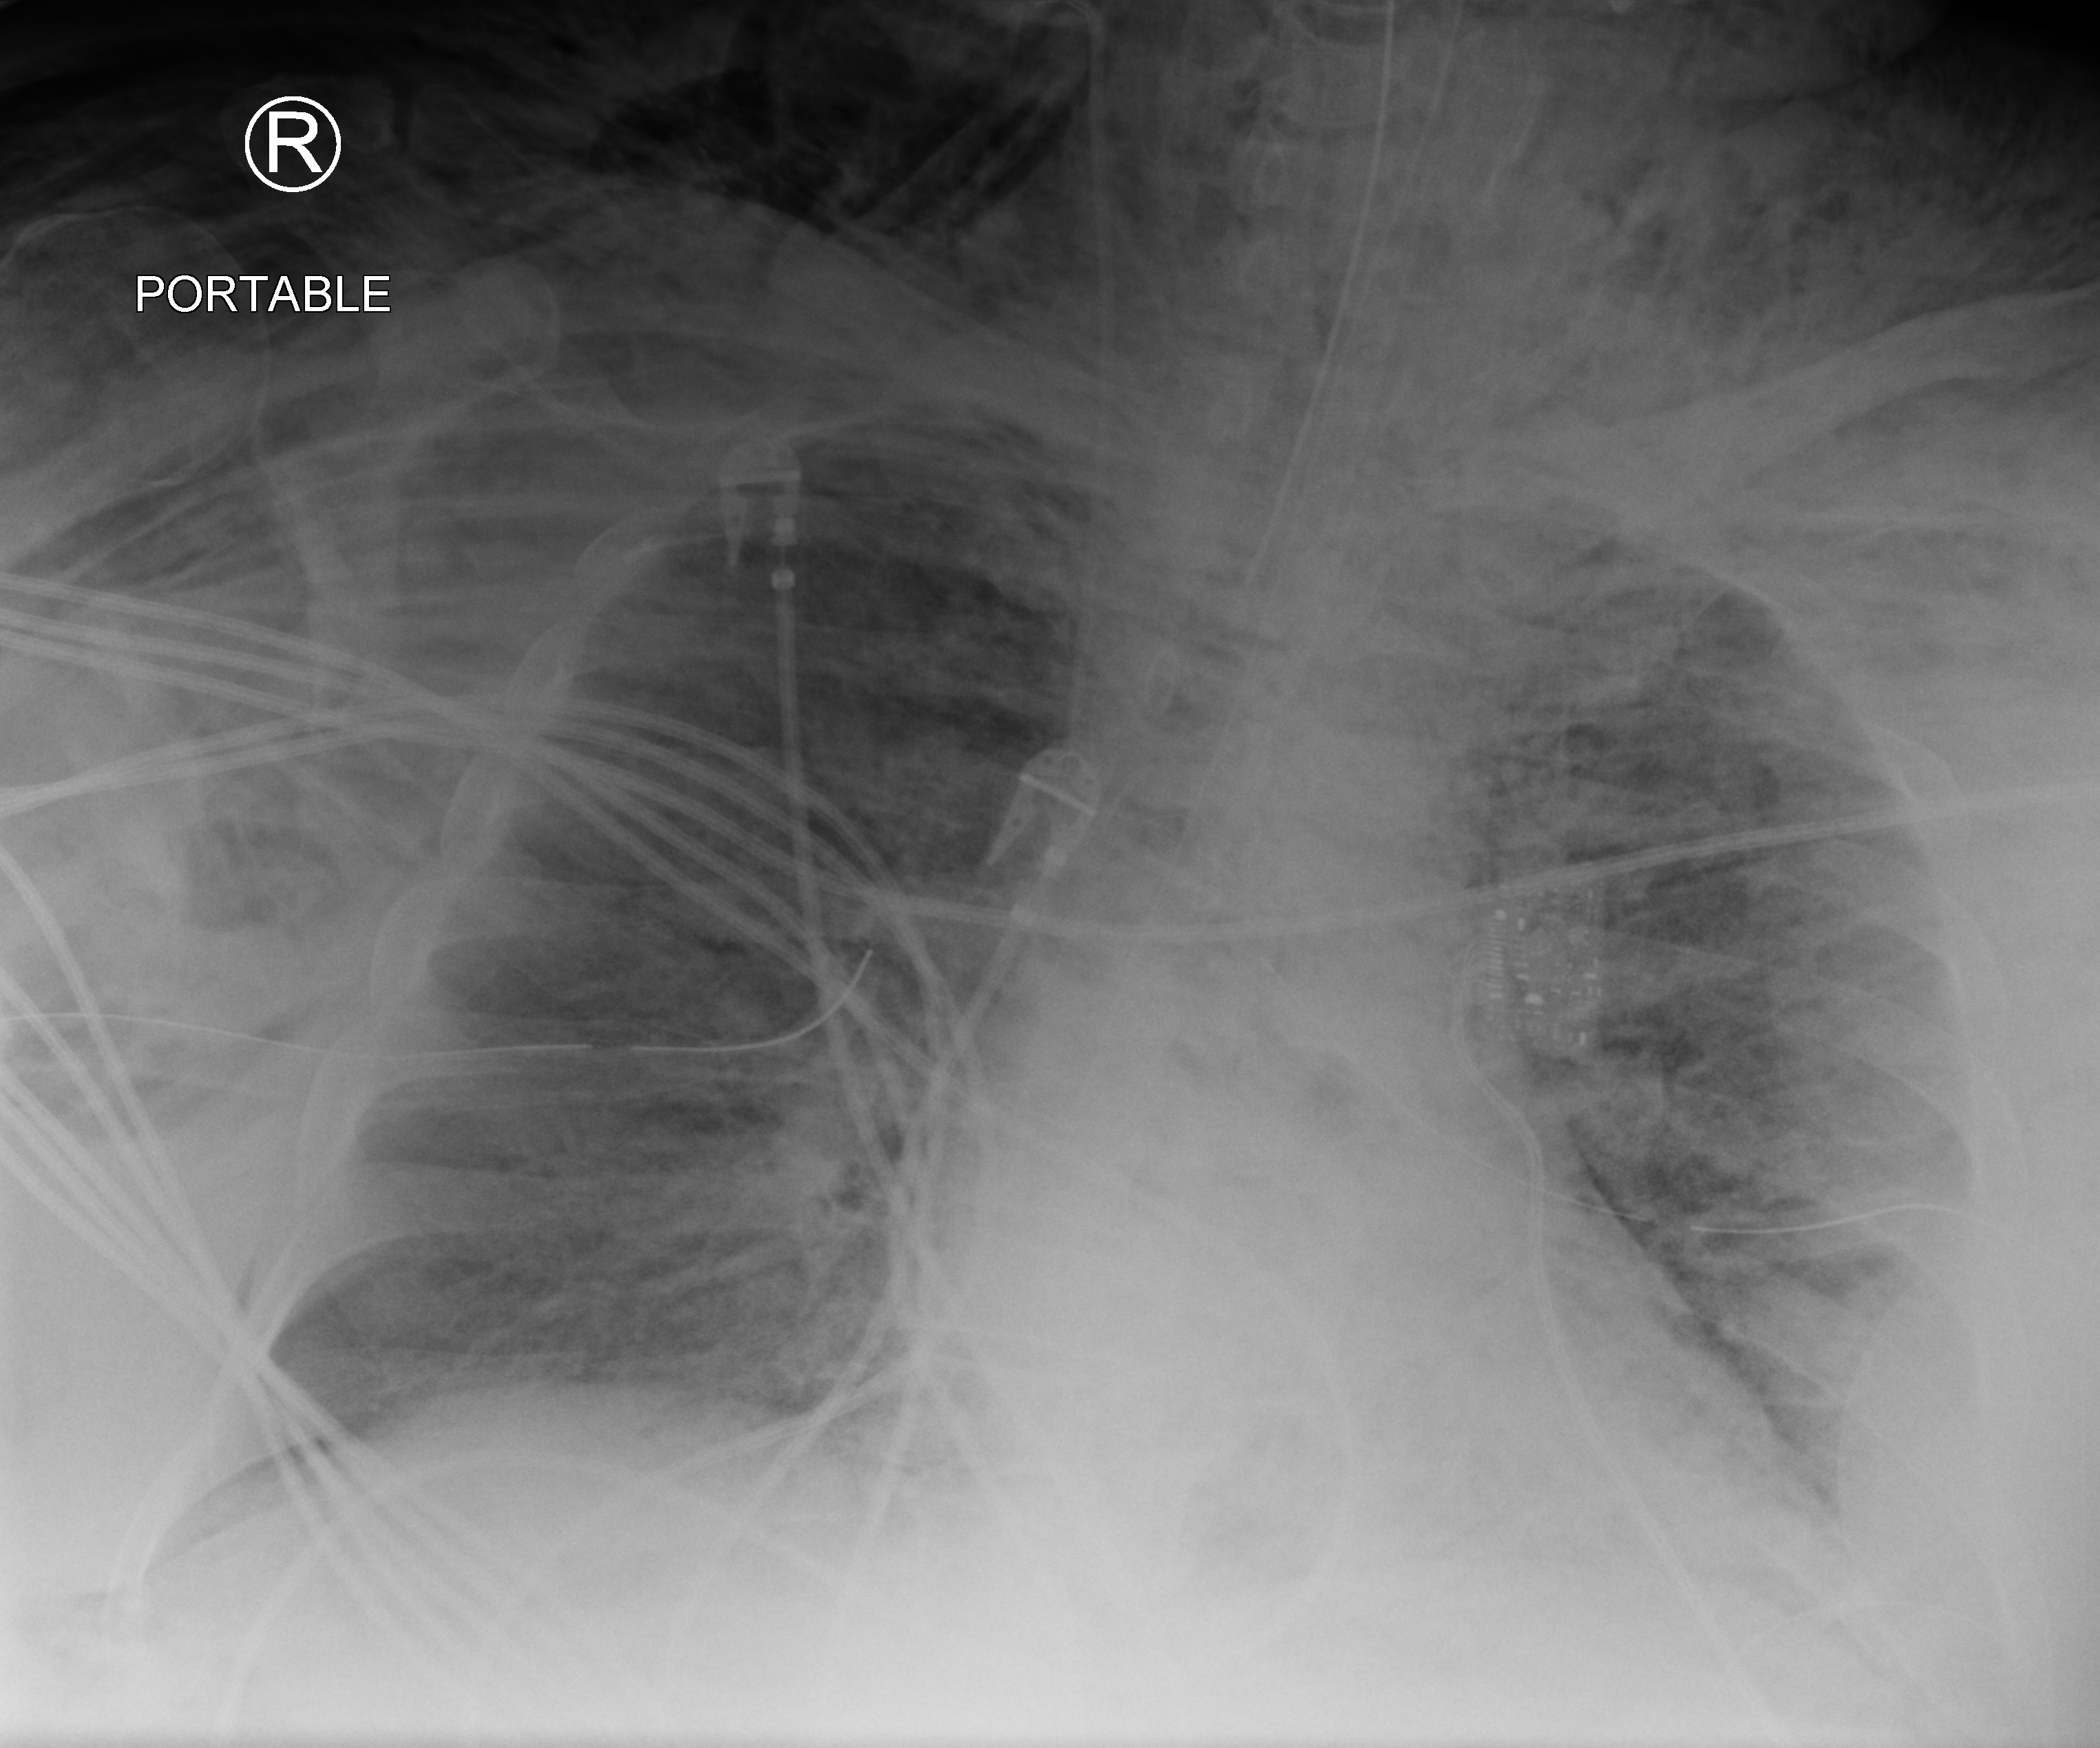
Bedside chest radiograph (computed radiography), anteroposterior (AP) projection. Adult patient hospitalised with COVID-19, age 18–59 years.
From the hospital-stay record, not from the radiograph (when in the stay this image was taken is not recorded):
- admitted to intensive care during this hospital stay: yes
- length of hospital stay: 26 days